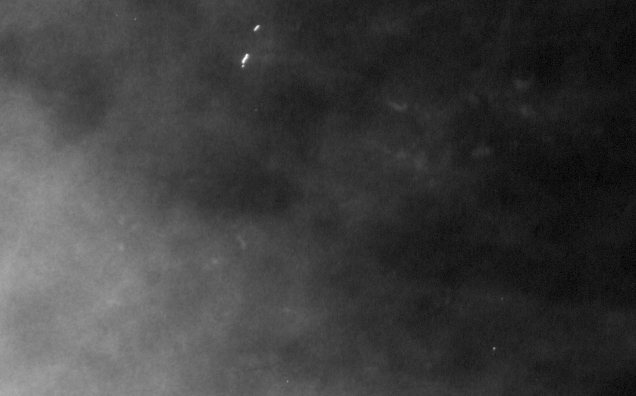
Crop from a digitized film mammogram around one marked abnormality, left breast, CC view.
Marked abnormality: calcifications, morphology pleomorphic, distribution linear; BI-RADS assessment category 4; subtlety rating 2 on a 1 (subtle) to 5 (obvious) scale; pathology result (as recorded, not read from the image): malignant.